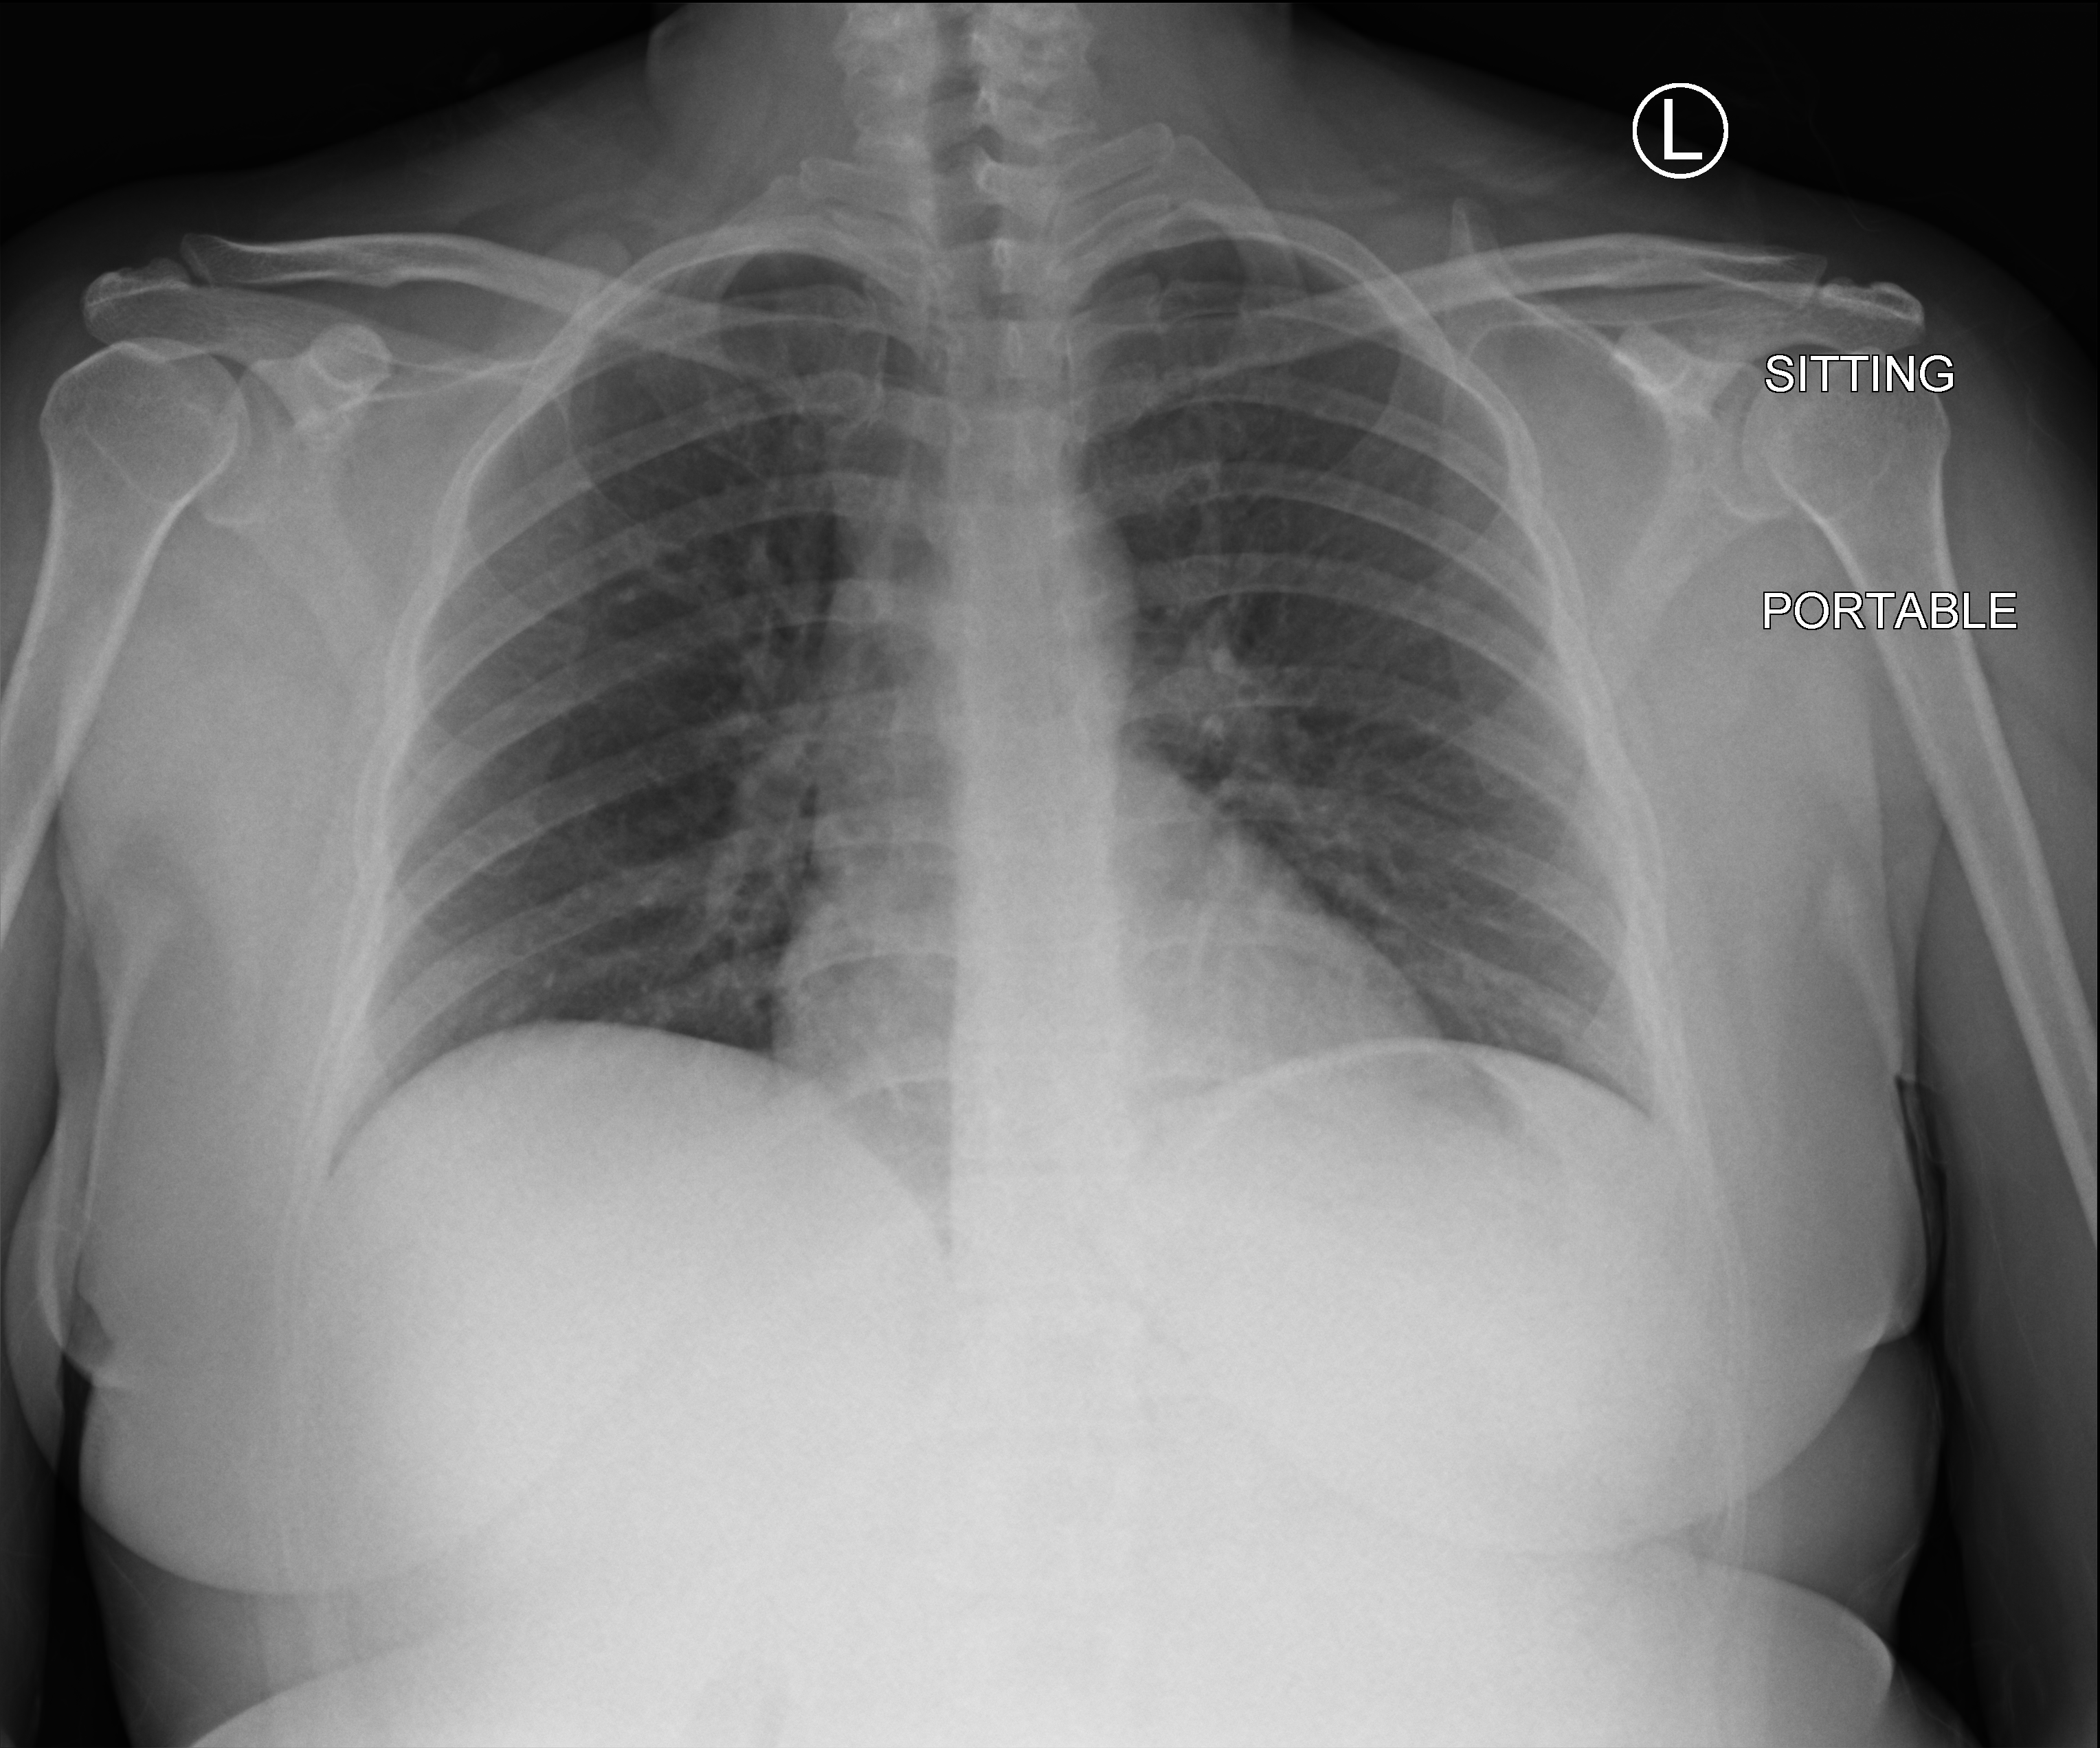
Chest X-ray (portable); anteroposterior (AP) projection. Female patient hospitalised with COVID-19, age 18–59 years.
Admission-level facts for this patient (not findings on this image; timing relative to this image not recorded): other chronic lung disease (admission record): yes; admitted to intensive care during this hospital stay: no; COPD (admission record): no.